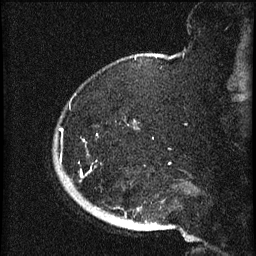
Breast MRI (dynamic contrast-enhanced), one sagittal slice. Slice 11 of 60 in the series (ordered by position). Dynamic contrast-enhanced series, image 2 of 3 at this slice position (ordered by acquisition). 1.5 T. TE 4.2 ms, TR 8.2 ms. 2 mm slice thickness. 256 × 256 image matrix, field of view 180 × 180 mm. Patient: female, 71 years.
Structures marked on this image (semi-automatic segmentation, software-assisted and operator-edited):
- analysis volume of interest (the breast-tissue region the enhancement analysis was run in; not a lesion): bounding box <54,116,136,196> (left, top, right, bottom; pixels)
- tumour enhancement mask (voxels above the 70 % enhancement threshold inside the analysis volume of interest): <59,129,85,177>